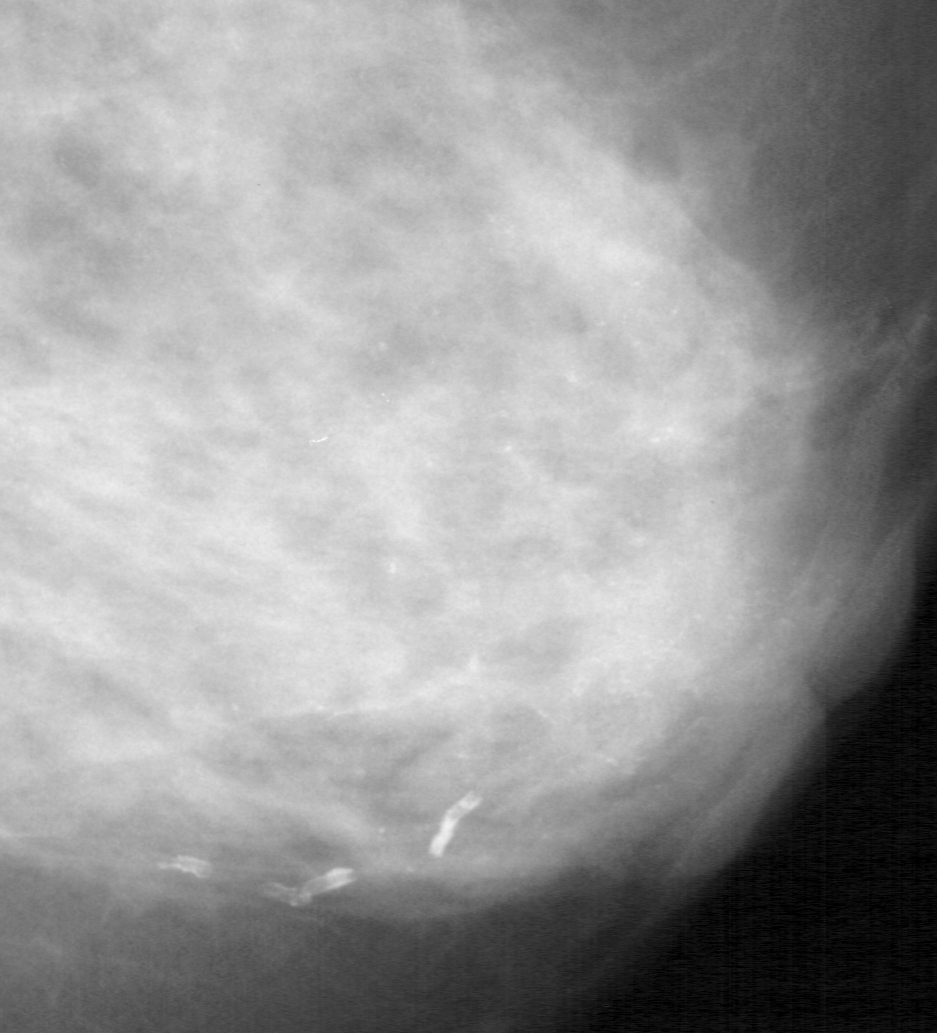
Crop from a digitized film mammogram around one marked abnormality; right breast; MLO view.
Marked abnormality: calcifications, morphology punctate / amorphous, distribution regional; BI-RADS assessment category 4; subtlety rating 3 on a 1 (subtle) to 5 (obvious) scale; pathology result (as recorded, not read from the image): benign.